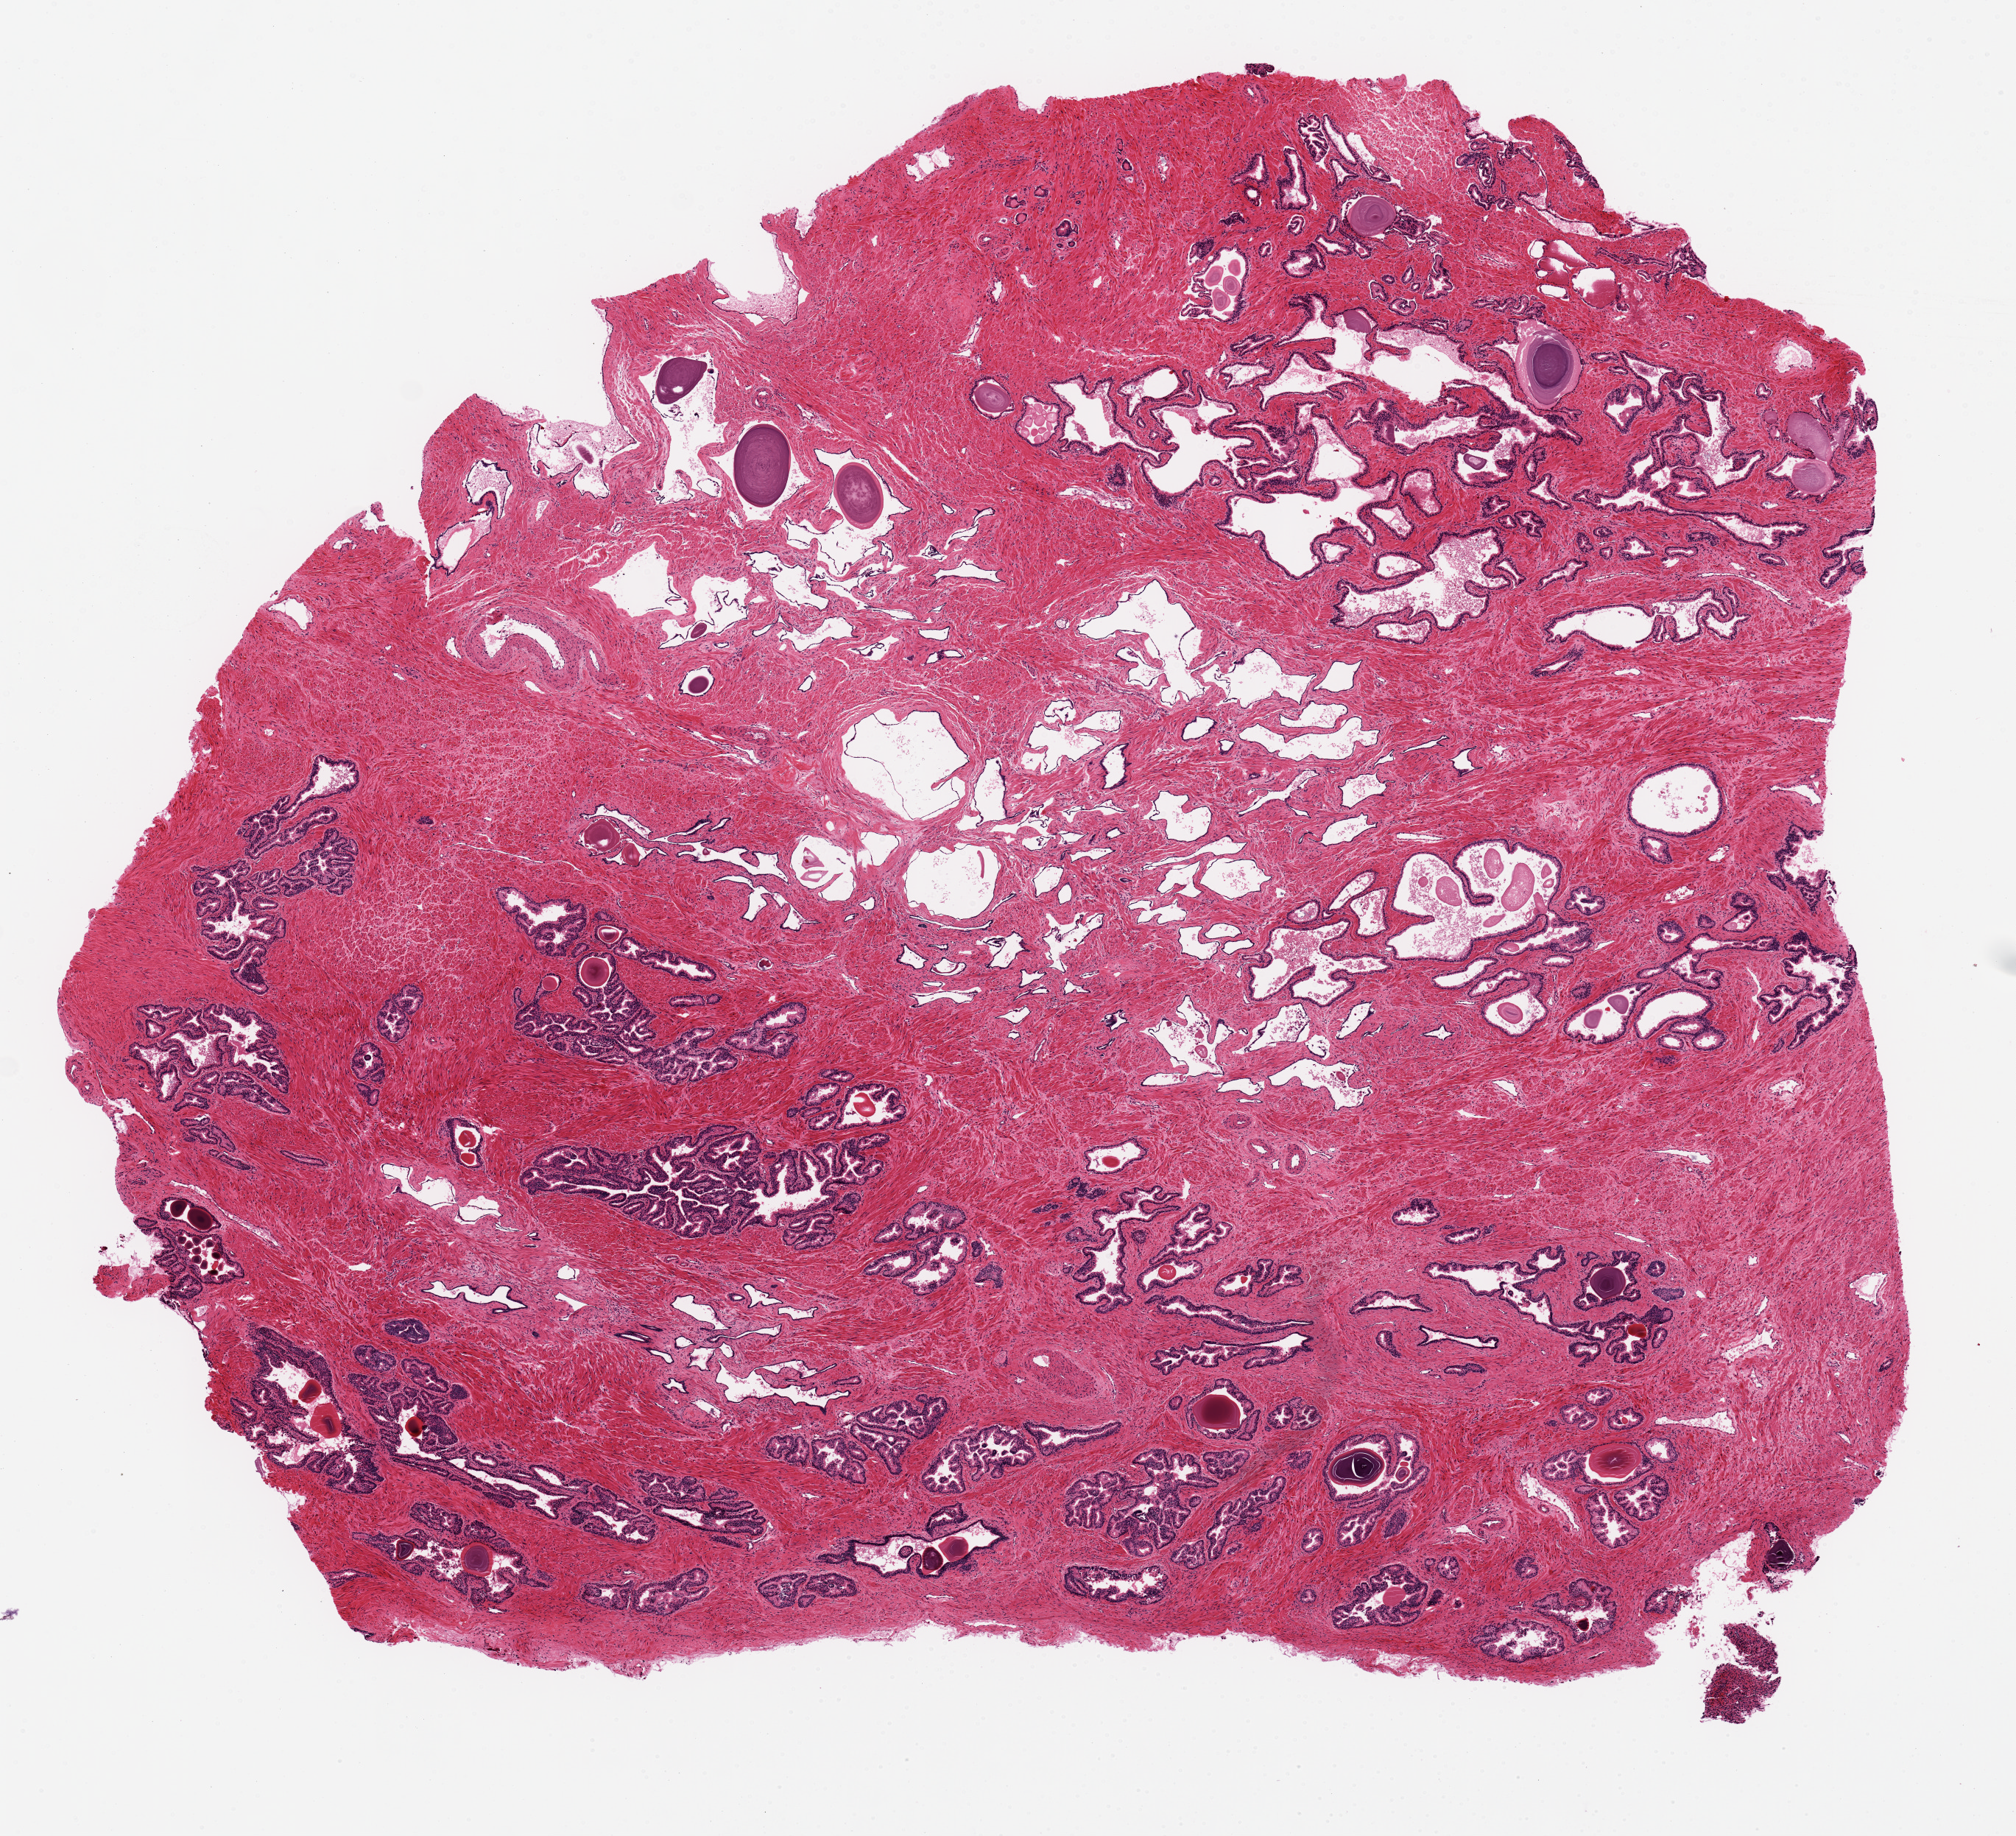
Digitized haematoxylin and eosin-stained section, brightfield, a low-resolution overview of the entire scanned area, about 10.8 x 9.9 mm. PAXgene-fixed, paraffin-embedded tissue. Section of prostate (target tissue). Donor tissue sample.
Reviewer comment on this tissue sample: Mixed atrophy and hyperplasia.